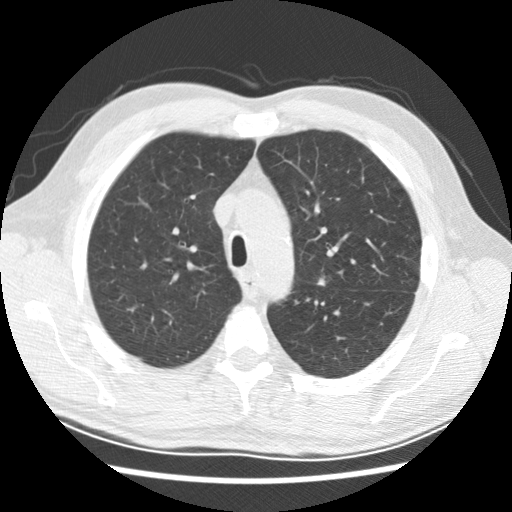
Axial slice from a low-dose chest CT screening exam; first (baseline) screen; lung window (W 1500 / L -600 HU); 2.5 mm slice thickness; slice 60 of 236 in the series; 512 × 512 image matrix, field of view 340 × 340 mm. Male, age 59 years at enrolment. Current smoker at enrolment.
Lesion marked by an expert reader, bounding box <302,268,342,296> (left, top, right, bottom; pixels). Screening reader's record for this exam (one nodule recorded; not confirmed to be the boxed lesion): non-calcified nodule or mass ≥4 mm, left upper lobe, 8 × 5 mm, smooth margins, soft tissue attenuation. Official screen result: positive, change unspecified: nodule(s) >= 4 mm or enlarging nodule(s), mass(es), or other non-specific abnormalities suspicious for lung cancer. Later outcome: lung cancer diagnosed 645 days after this screen (after the second annual screen) — adenocarcinoma, NOS, left upper lobe, left lower lobe, poorly differentiated (G3), stage IV (AJCC 6th edition).